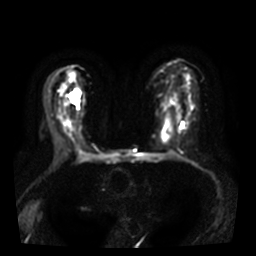
Breast MRI, one axial slice; position 19 of 38 along the scan axis; diffusion-weighted series; image 2 of 4 stored at this slice position (different b-values; order by instance number); 3 T; 5 mm slice thickness; 256 × 256 image matrix. Female patient.
Annotated regions visible in this slice (manually delineated by an expert):
- tumour on diffusion-weighted imaging: bounding box <70,91,80,108> (left, top, right, bottom; pixels)